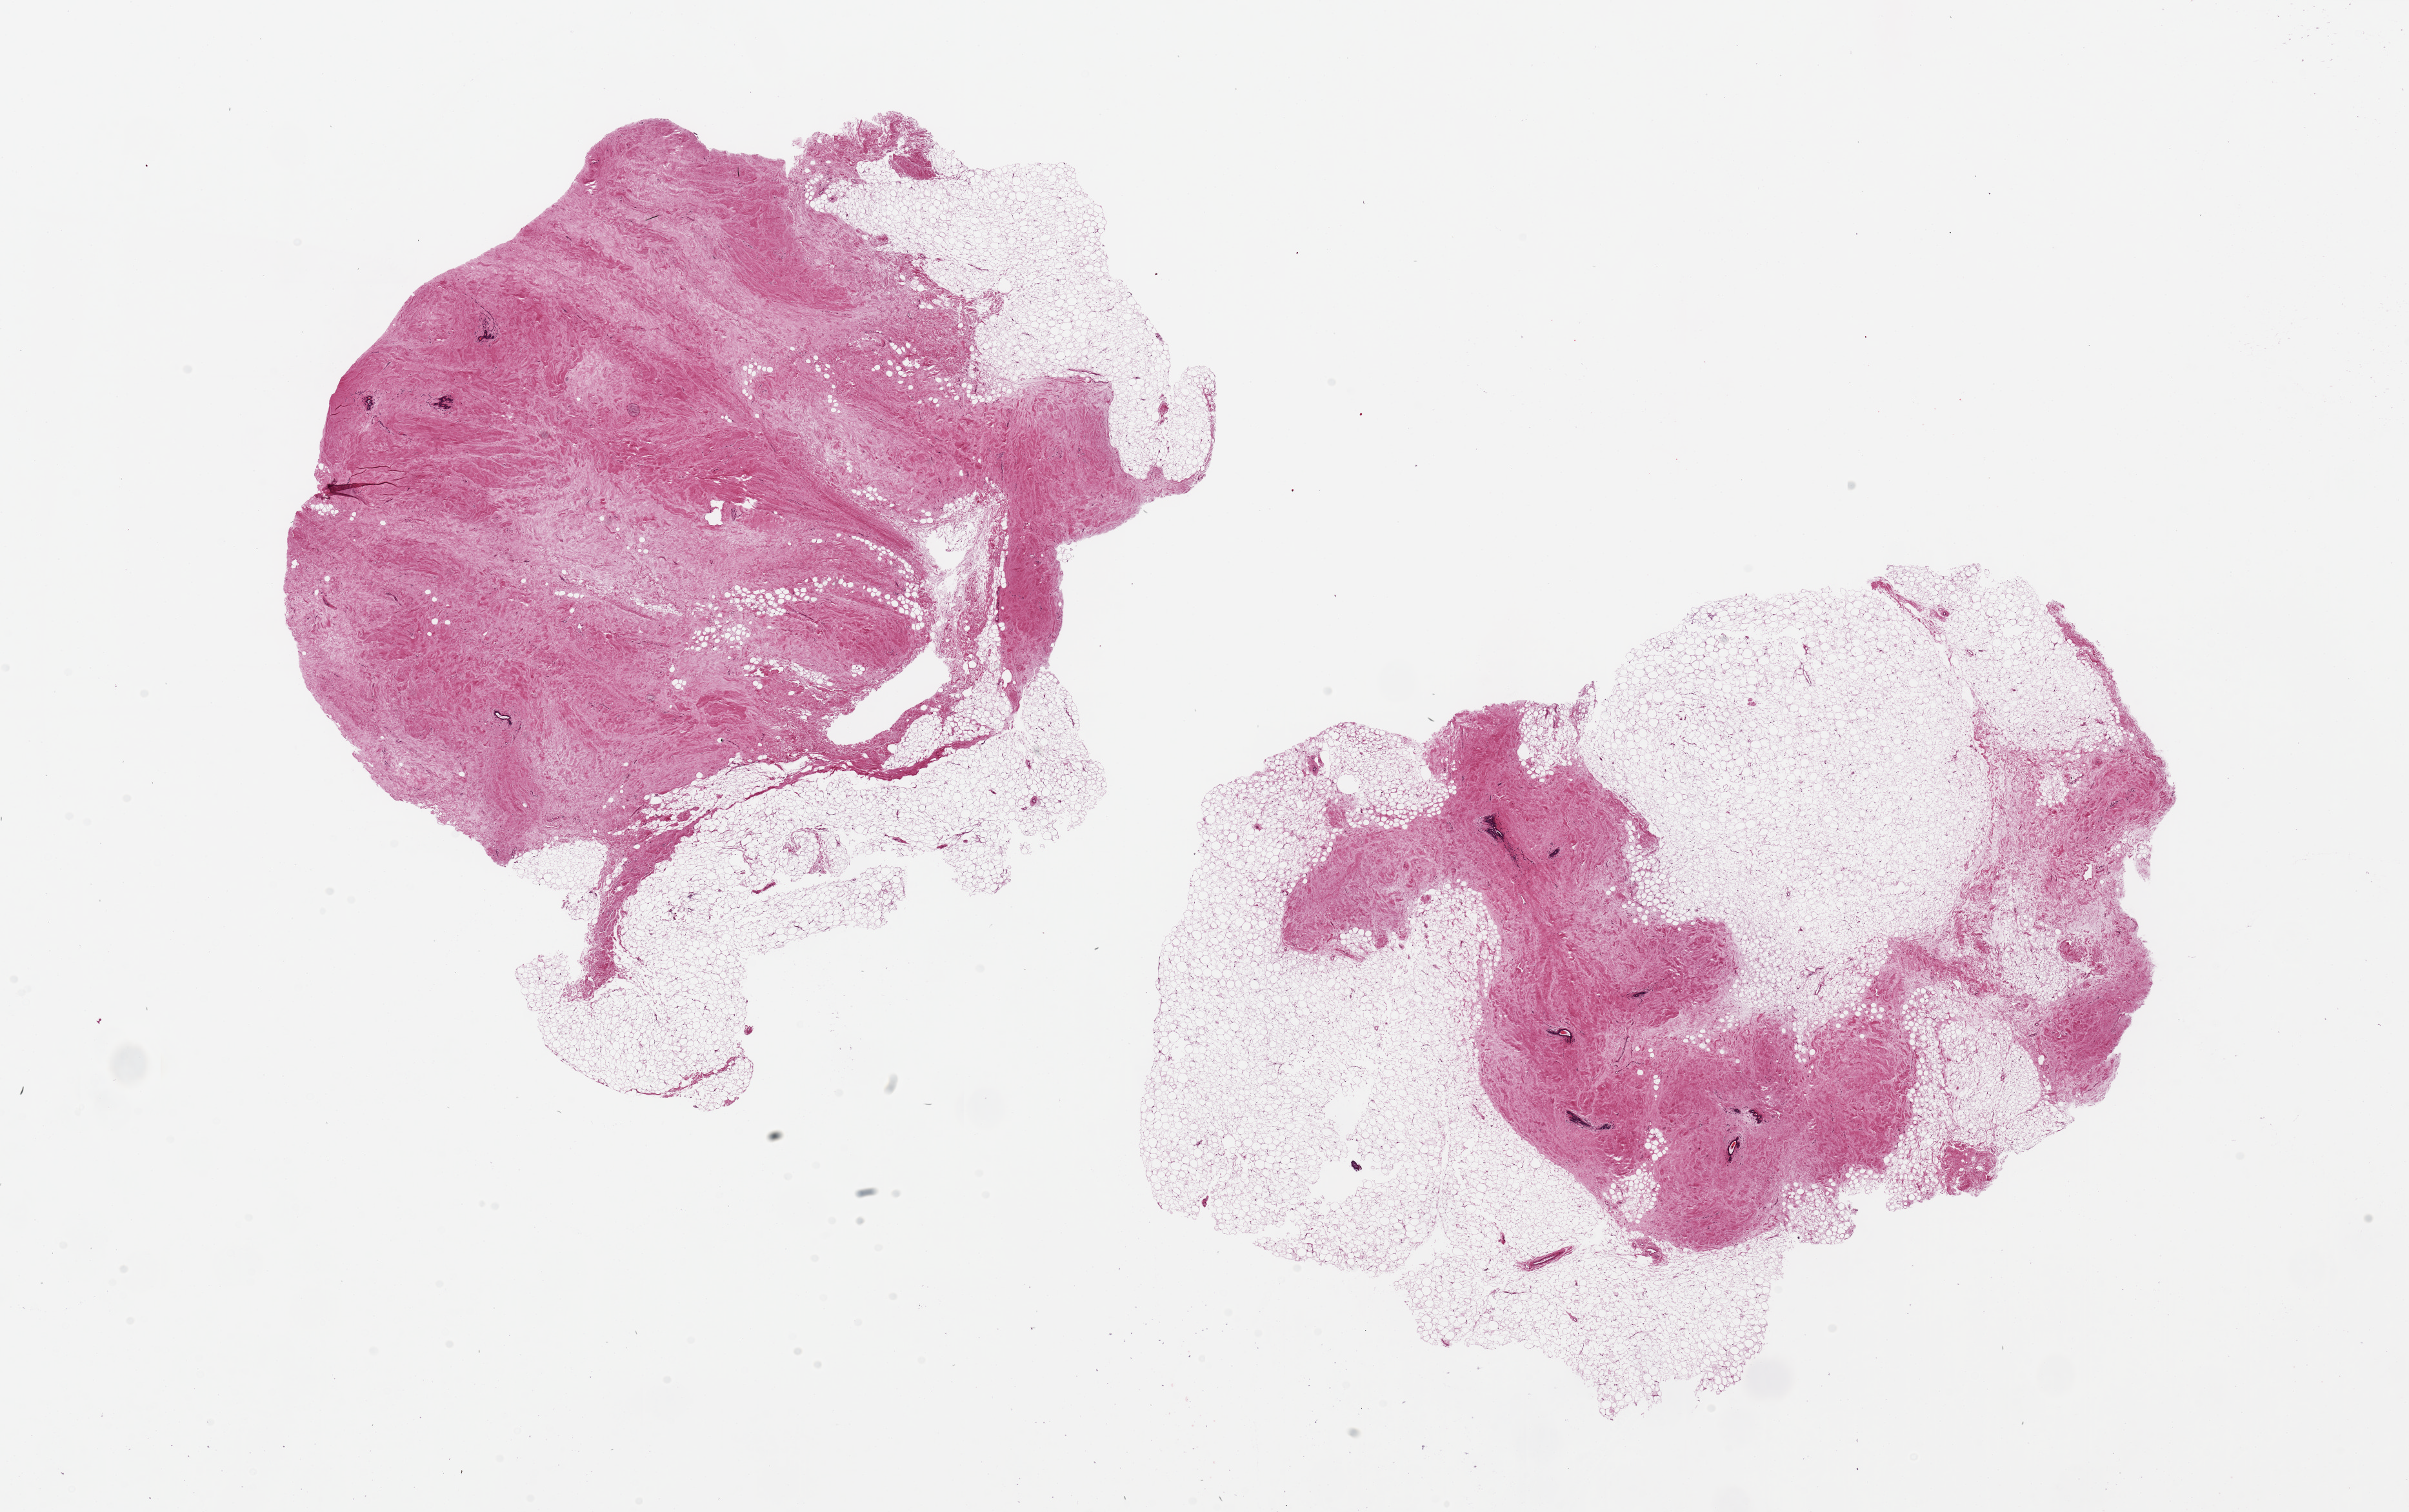
Whole-slide image, H&E stain — low-resolution overview of the scanned area, about 29.5 x 18.5 mm; PAXgene-fixed paraffin-embedded (PFPE) section; sampled site (target tissue): breast; donor tissue sample. Donor sex: female.
Reviewer comment on this tissue sample: 2 pieces, 12x11 & 13x9.5mm; 1 fibrous, 1 fatty; ducts, few lobules, atrophic.